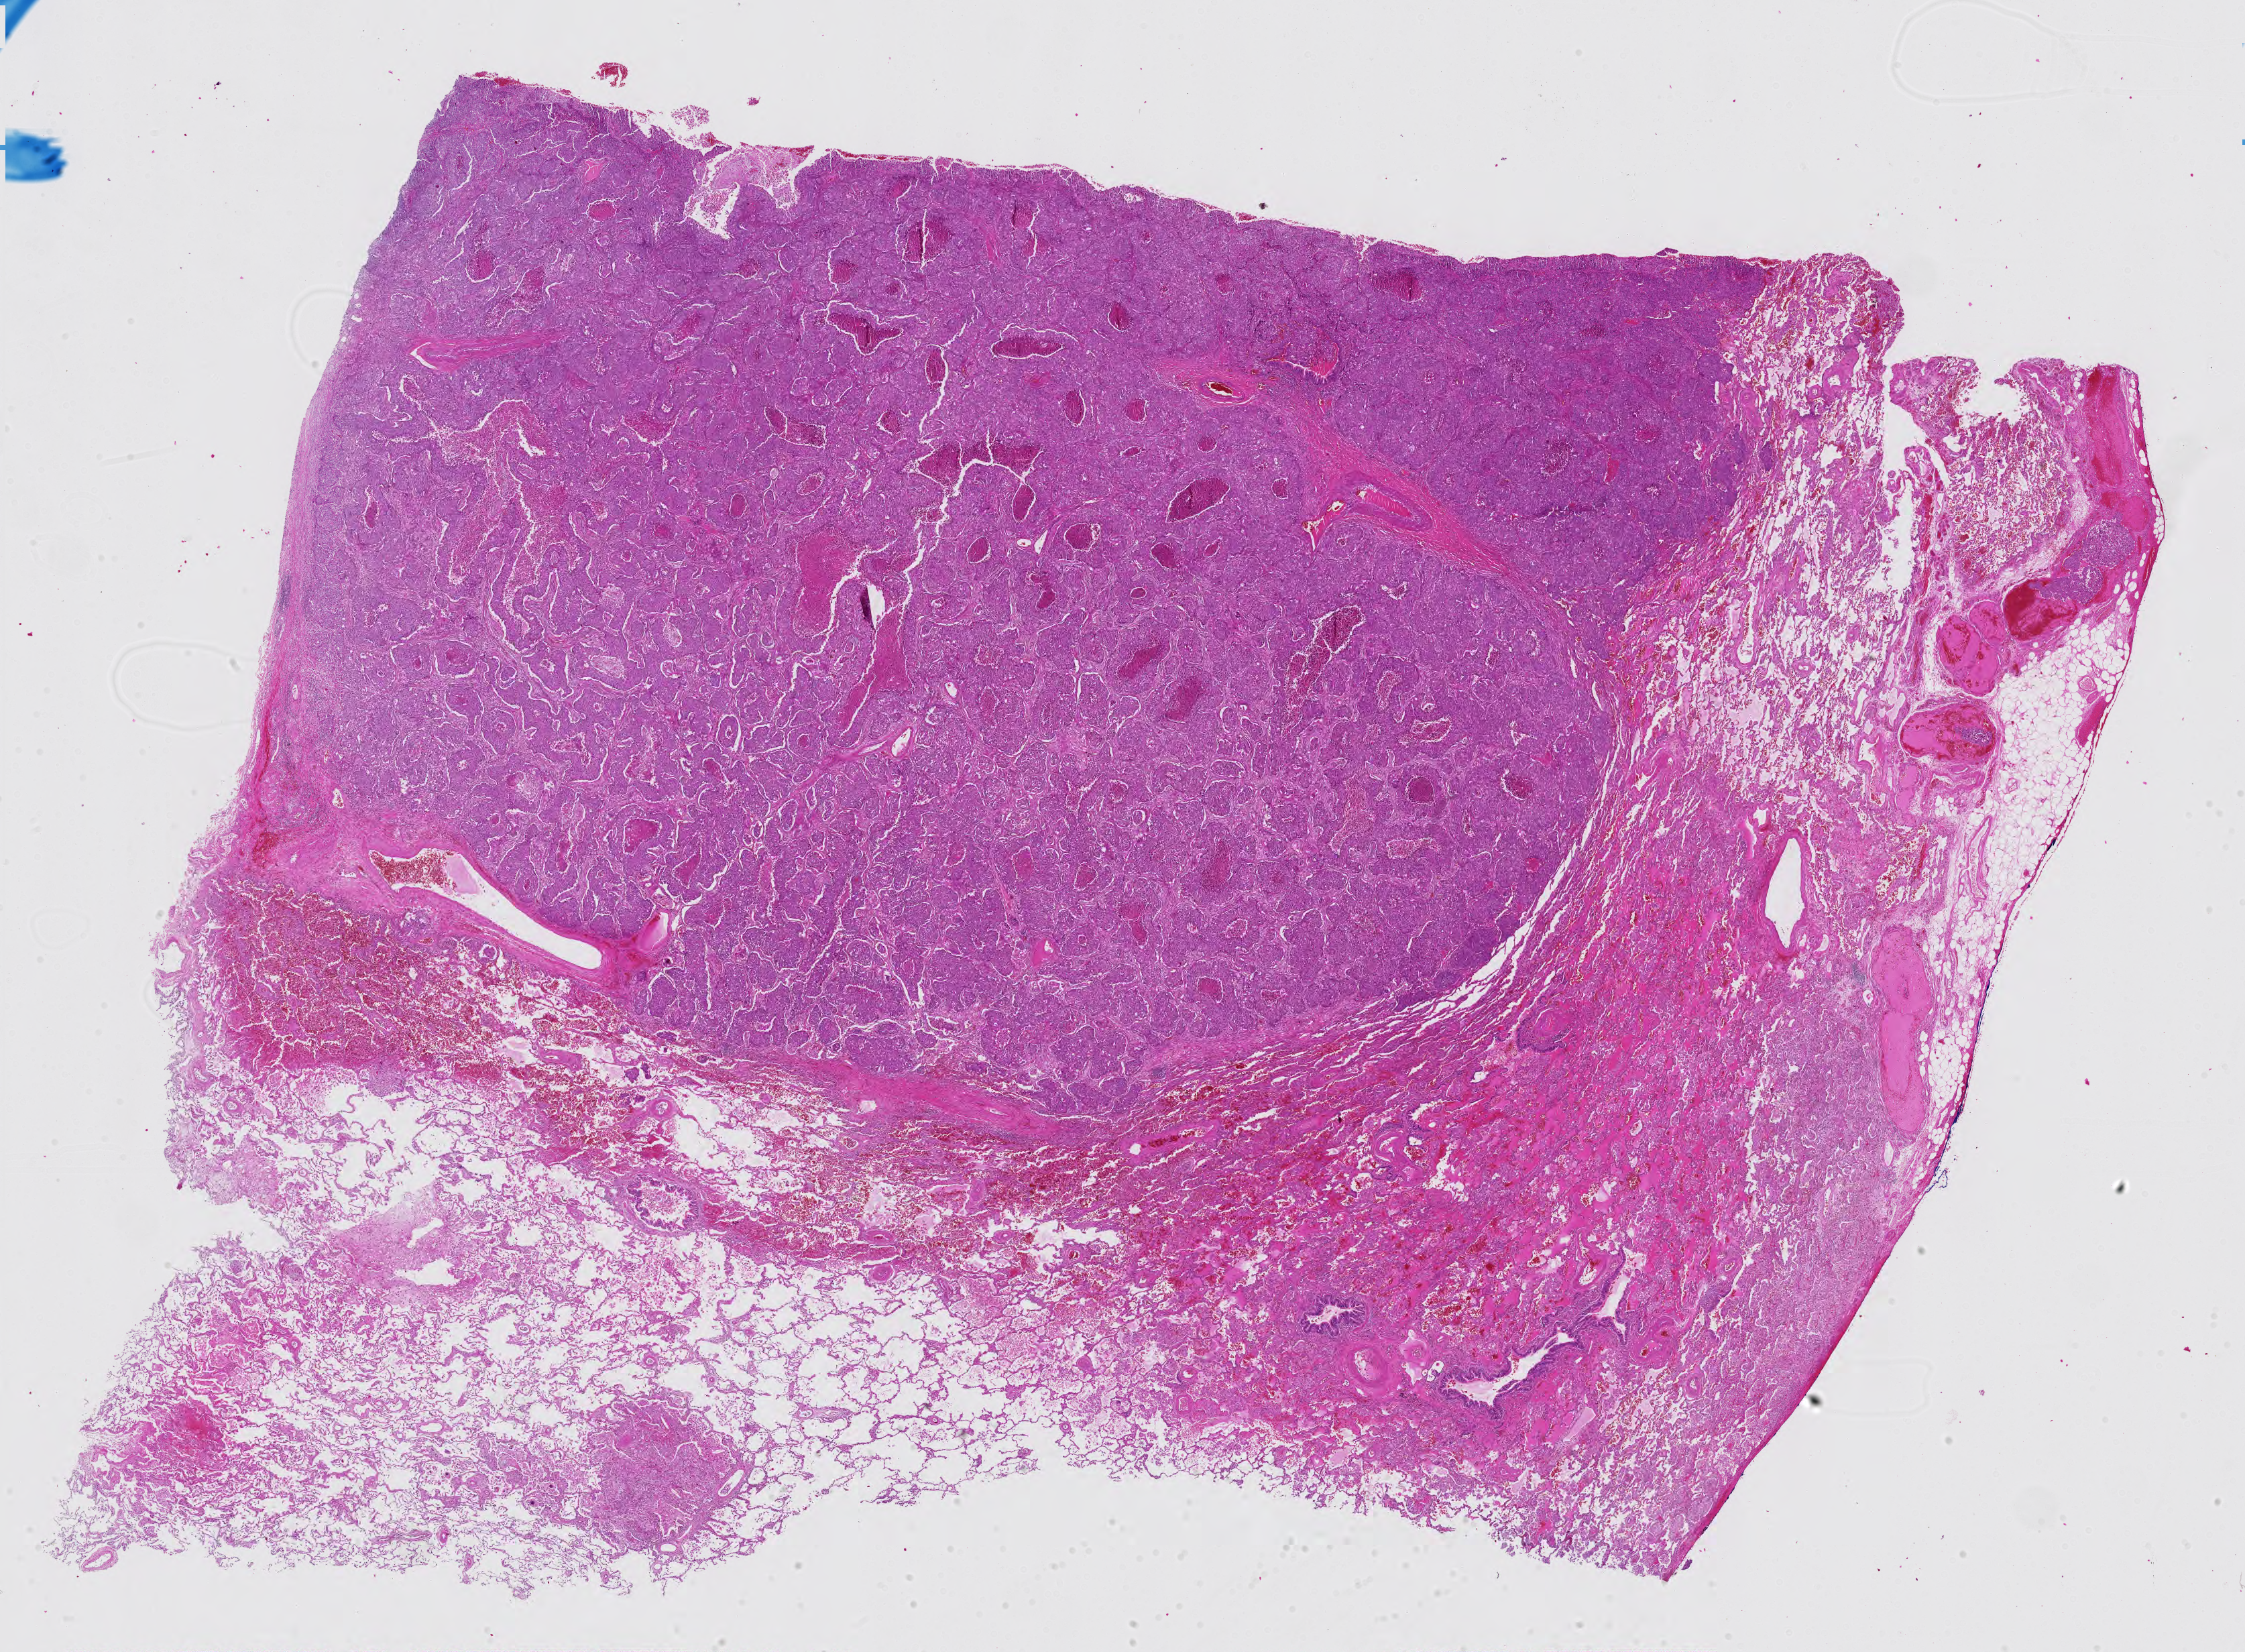
H&E-stained whole-slide image, whole scanned area (about 24.3 x 17.9 mm, acquisition: 40x scan) shown as a low-resolution overview; FFPE section; primary tumour sample from the lung. Patient: male, age at initial diagnosis 67 years.
AJCC pathologic stage: IIA (7th edition). Diagnosis: Adenocarcinoma, NOS.